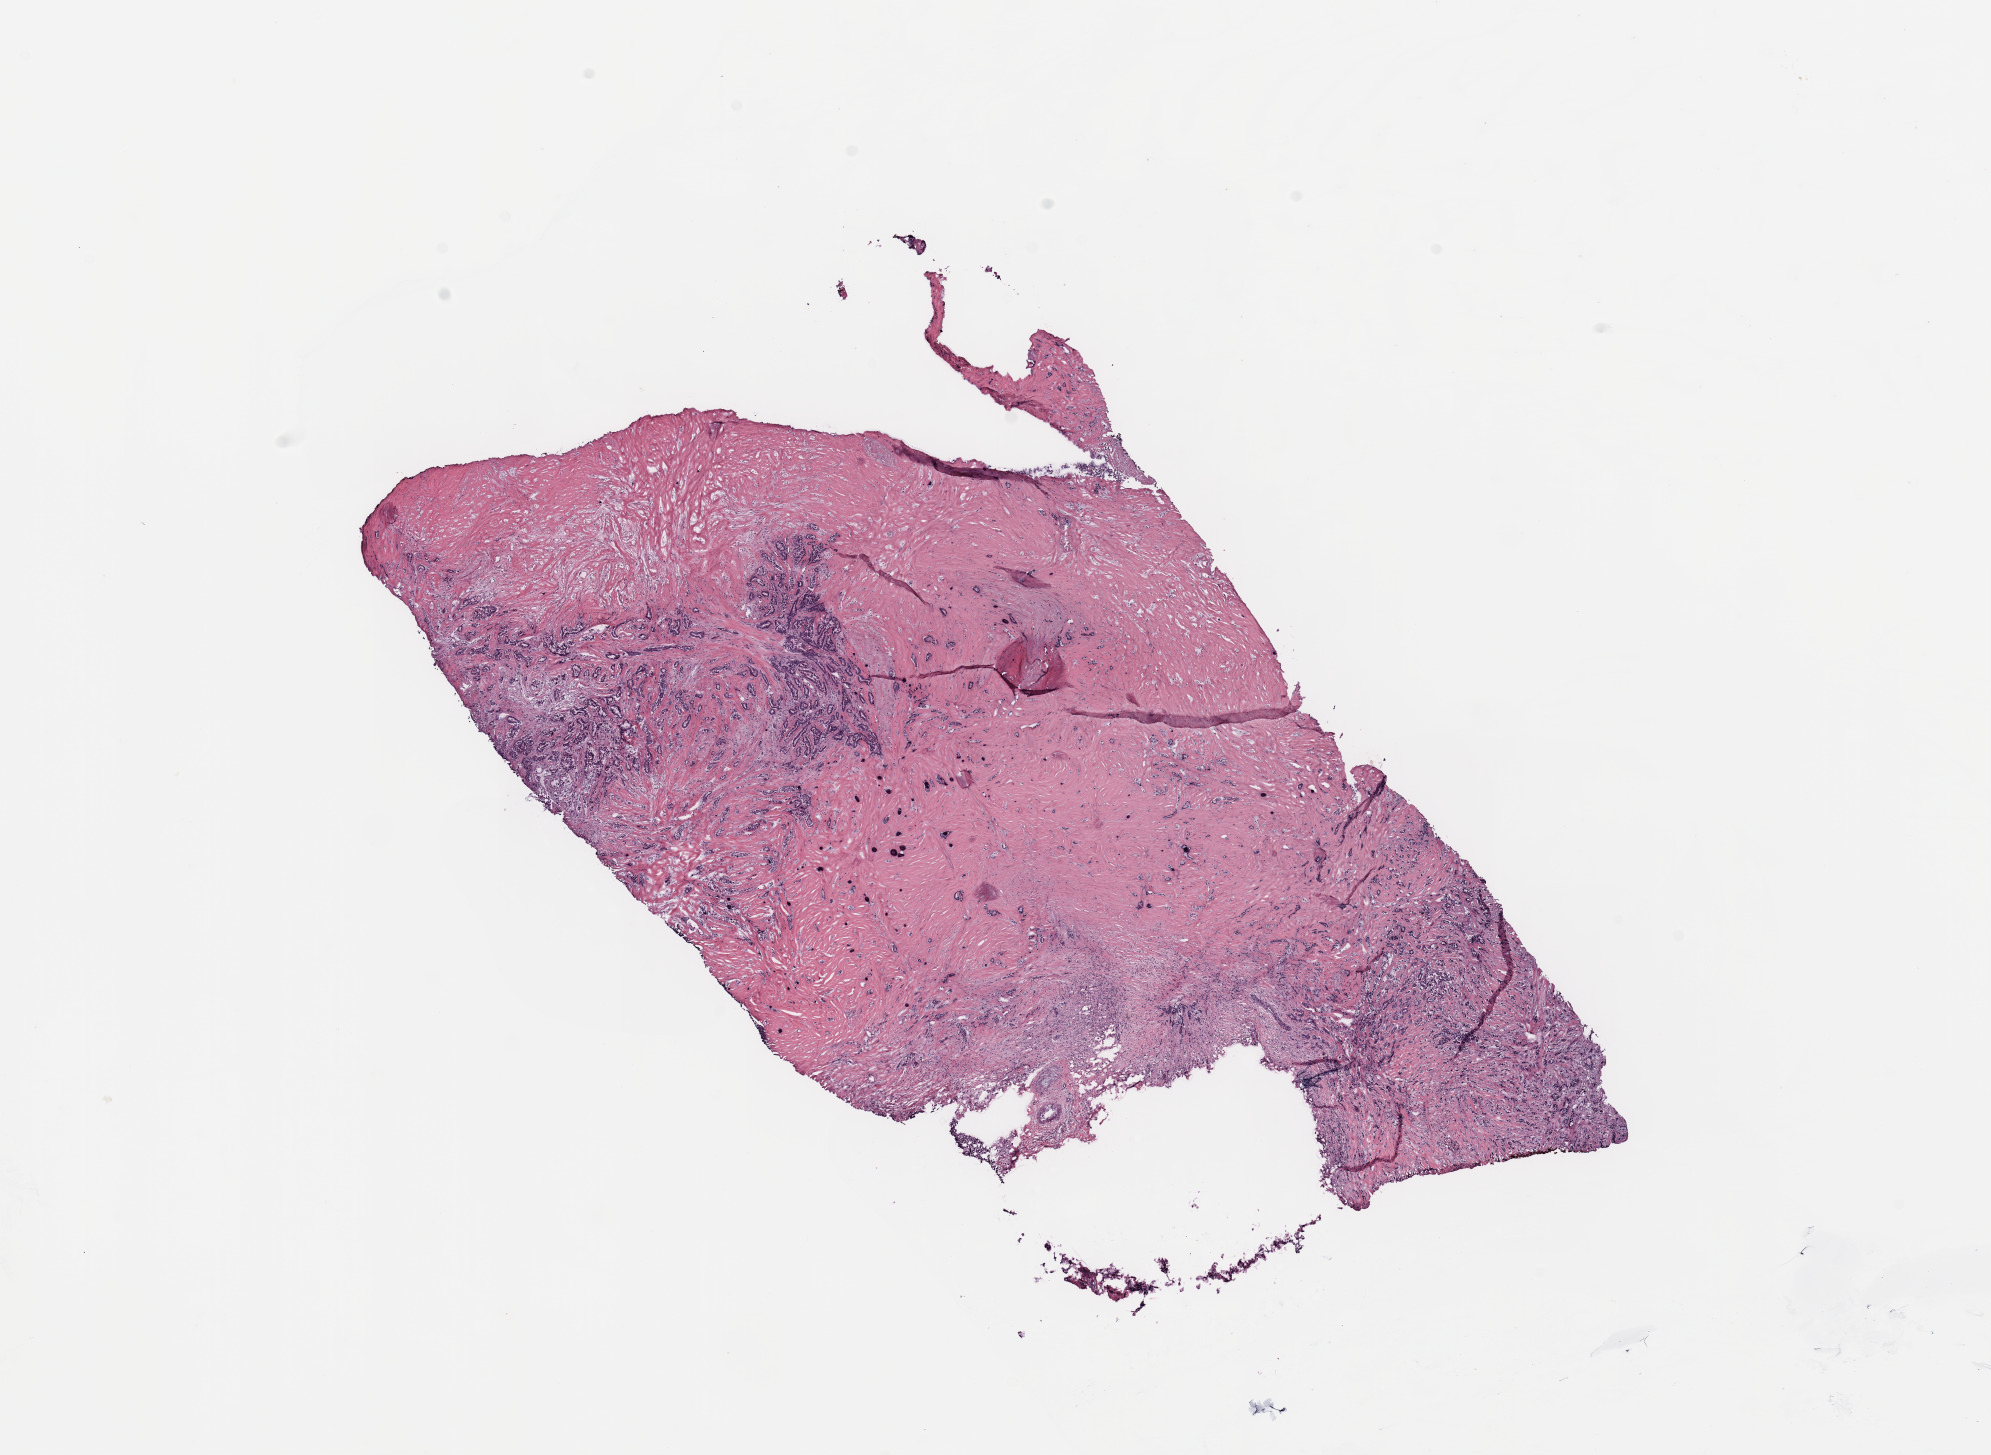
Digitized Hematoxylin and eosin (H&E) stained tissue section (whole slide), a low-resolution overview of the entire scanned area, about 15.8 x 11.5 mm, tumour tissue sample, breast. Patient: female, age 50 years.
Histologic diagnosis: Infiltrating duct carcinoma, NOS. AJCC pathologic stage: IA.